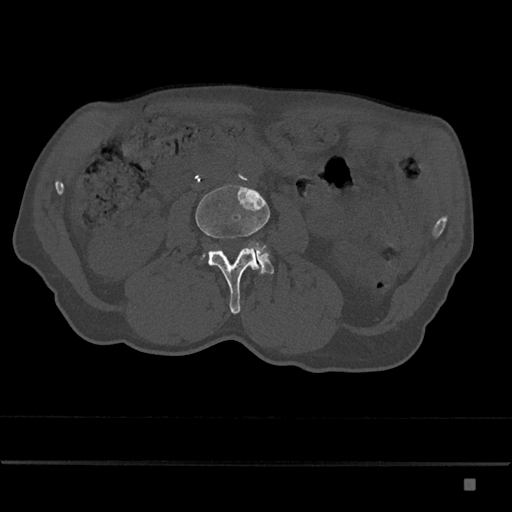
CT including the spine, one axial slice. Position 392 of 797 along the scan axis. Reconstruction kernel Br40s/3. Bone window (W 1800 / L 400 HU). 512 × 512 image matrix, field of view 390 × 390 mm. Male patient, age 72 years. From the clinical record (not read from this slice): primary cancer: prostate.
Annotated regions visible in this slice (semi-automatic segmentation, software-assisted and operator-edited):
- L3 vertebra: bounding box <195,185,270,314> (left, top, right, bottom; pixels)
- L4 vertebra: <203,244,274,274>